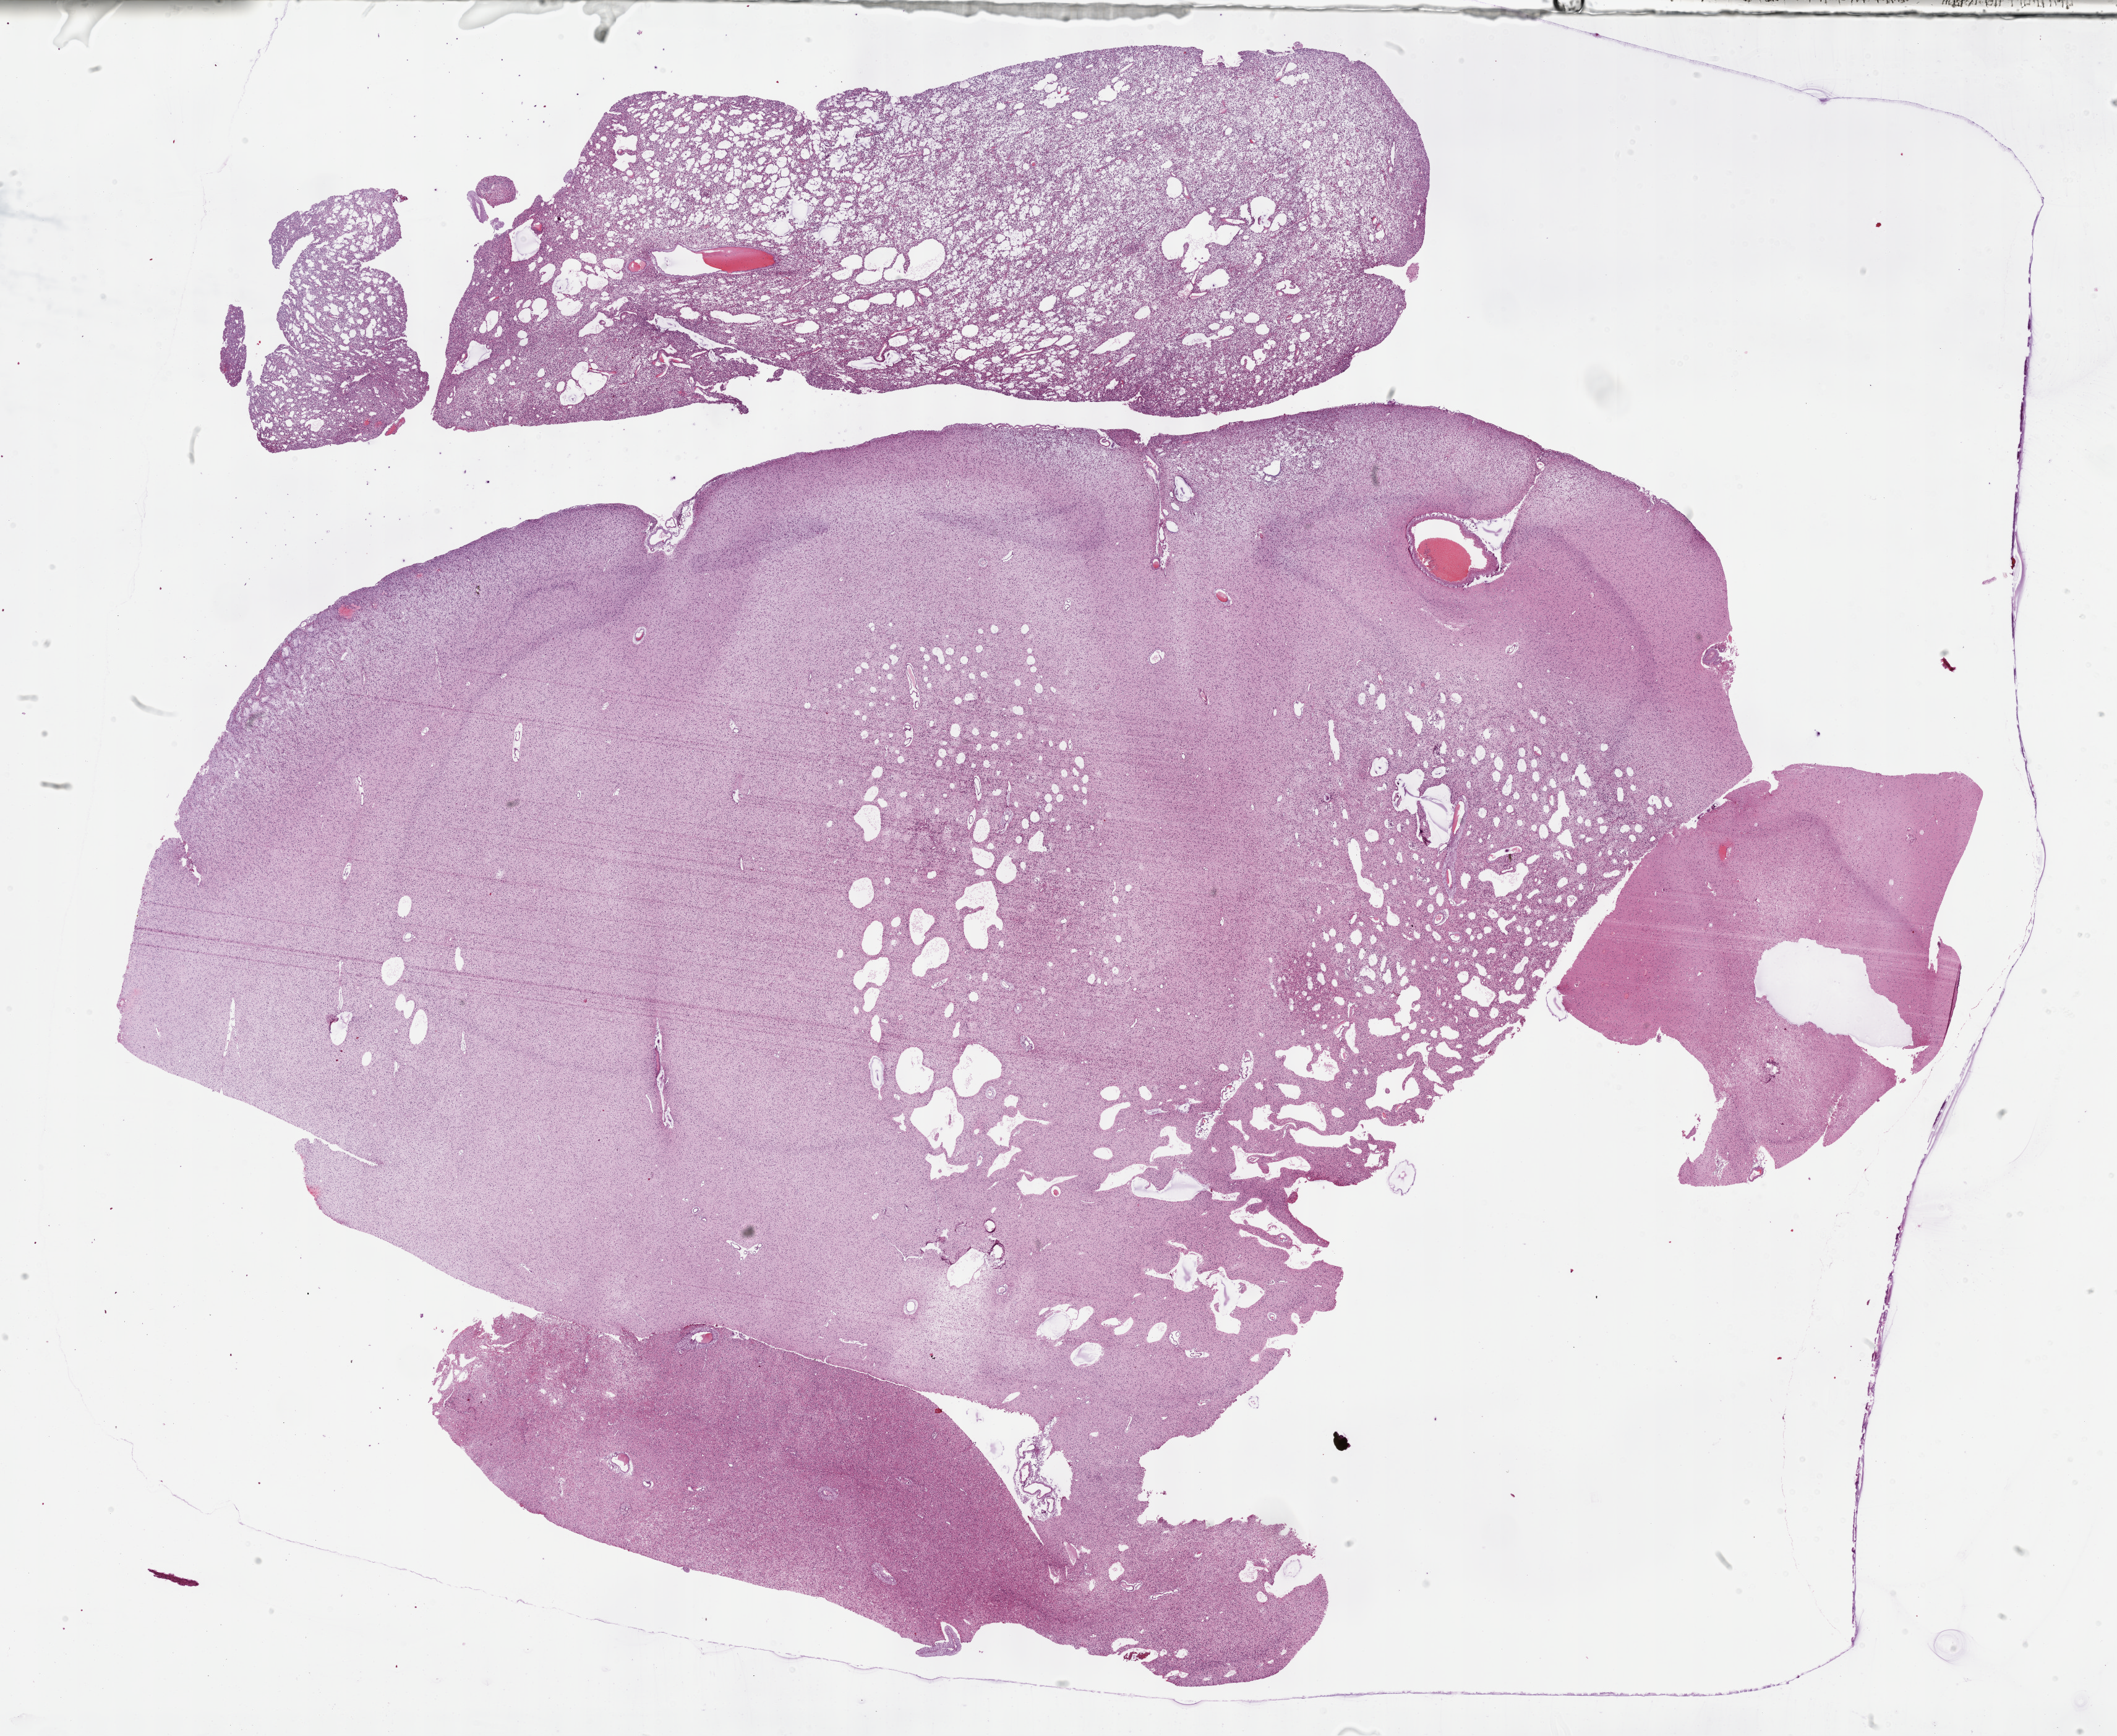
Digitized H&E-stained tissue section (whole slide), shown as a low-resolution overview of the whole scanned area (about 27.7 x 22.7 mm, acquisition: 40x scan). Formalin-fixed paraffin-embedded (FFPE) diagnostic section. Brain, primary tumour sample. Female patient; age at initial diagnosis 38 years. Histologic grade: G3 (poorly differentiated).
Laterality: right. Pathologic diagnosis: Mixed glioma.